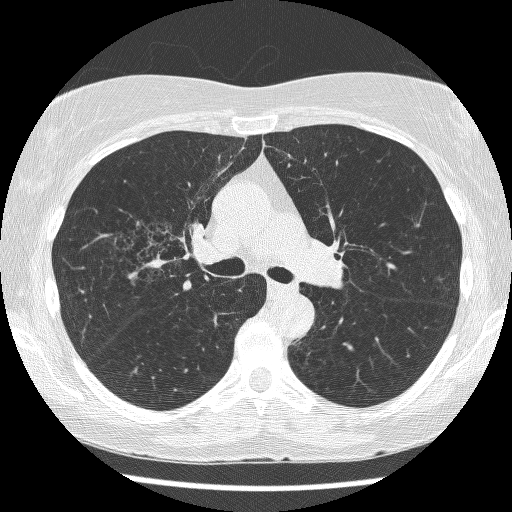
Chest CT (low-dose screening protocol), one axial image, first (baseline) screen, lung window (W 1500 / L -600 HU), 1.25 mm slice thickness, 120 kVp. Female, age 64 years at enrolment.
Expert-annotated lung lesion, bounding box [x1, y1, x2, y2] px = [125, 220, 204, 289]. The screening reader recorded 3 non-calcified nodules or masses ≥4 mm on this exam (right upper lobe, right upper lobe, left lower lobe); which of them this box marks is not recorded. Later outcome: lung cancer diagnosed 735 days after this screen (after the third annual screen) — adenocarcinoma, NOS, right upper lobe, right middle lobe, right hilum, stage IV (AJCC 6th edition), 85 mm at pathology.